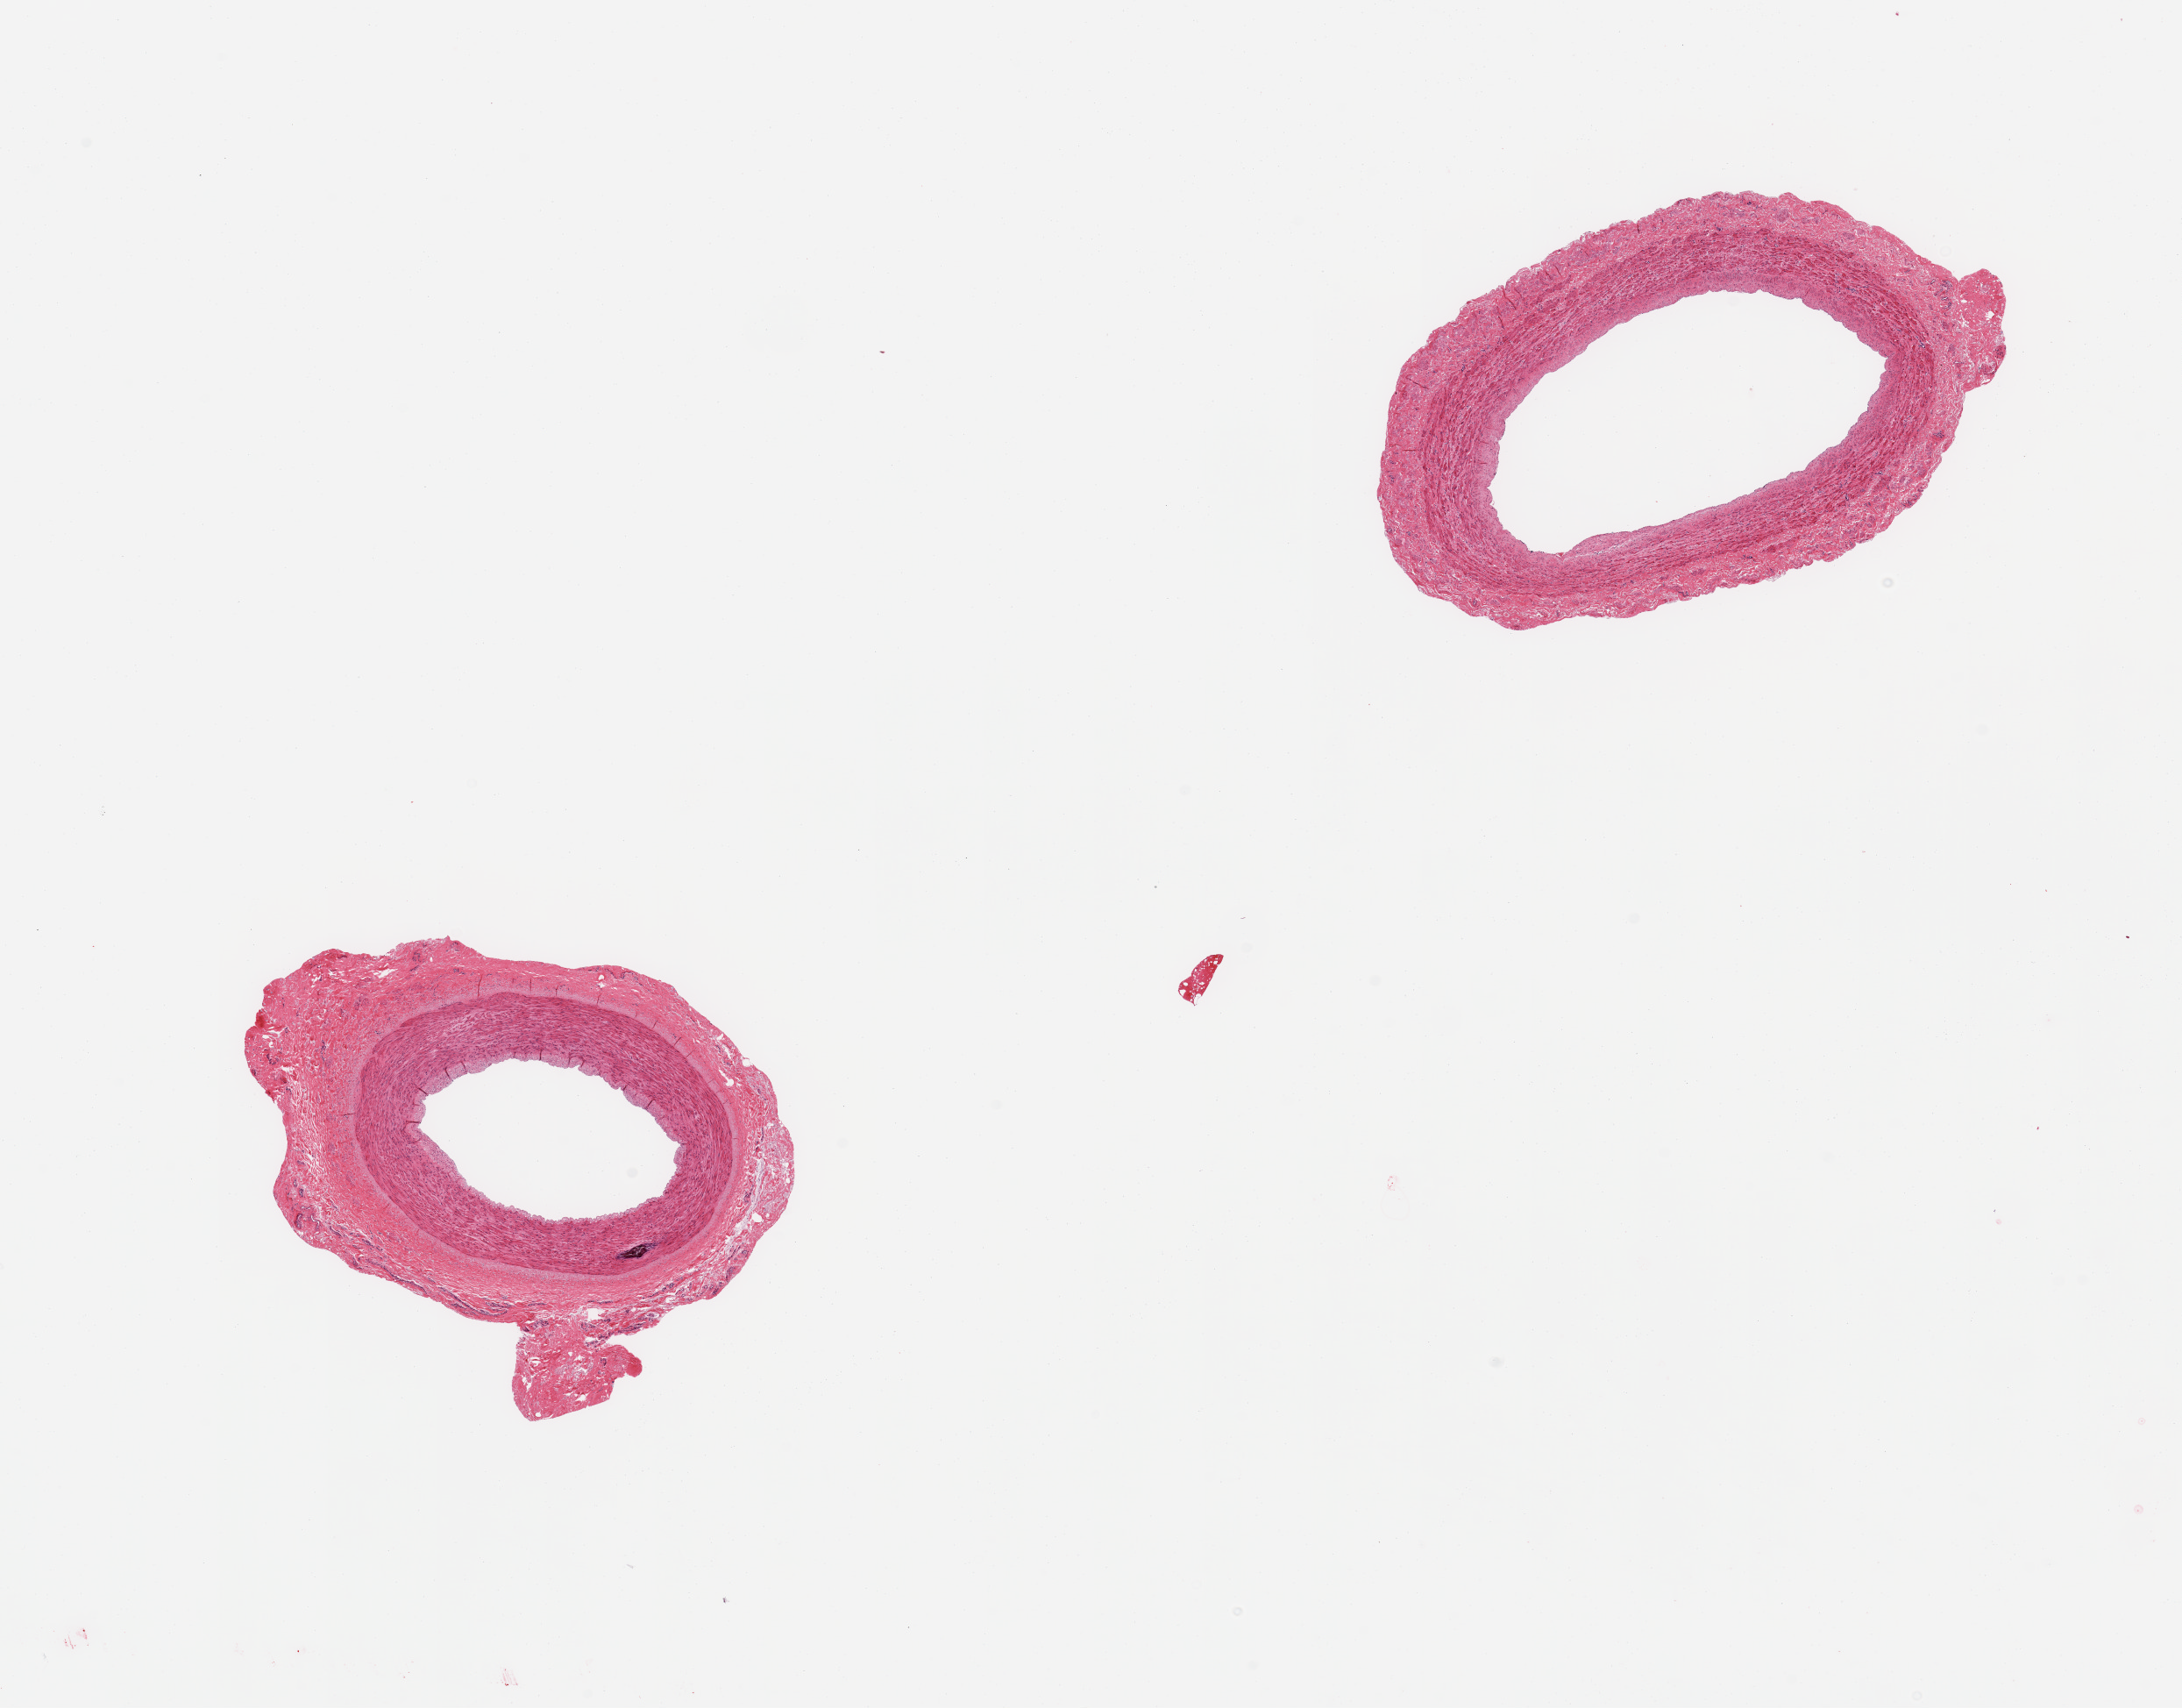
Whole-slide image, hematoxylin and eosin (H&E) stain, brightfield — a low-resolution overview of the entire scanned area, about 19.7 x 15.4 mm (acquisition: 20x scan). PAXgene-fixed, paraffin-embedded tissue. Sampled site (target tissue): tibial artery. Donor tissue sample.
Pathologist's review note for this sample: 2 pieces, no significant atherosis or adherent fat.